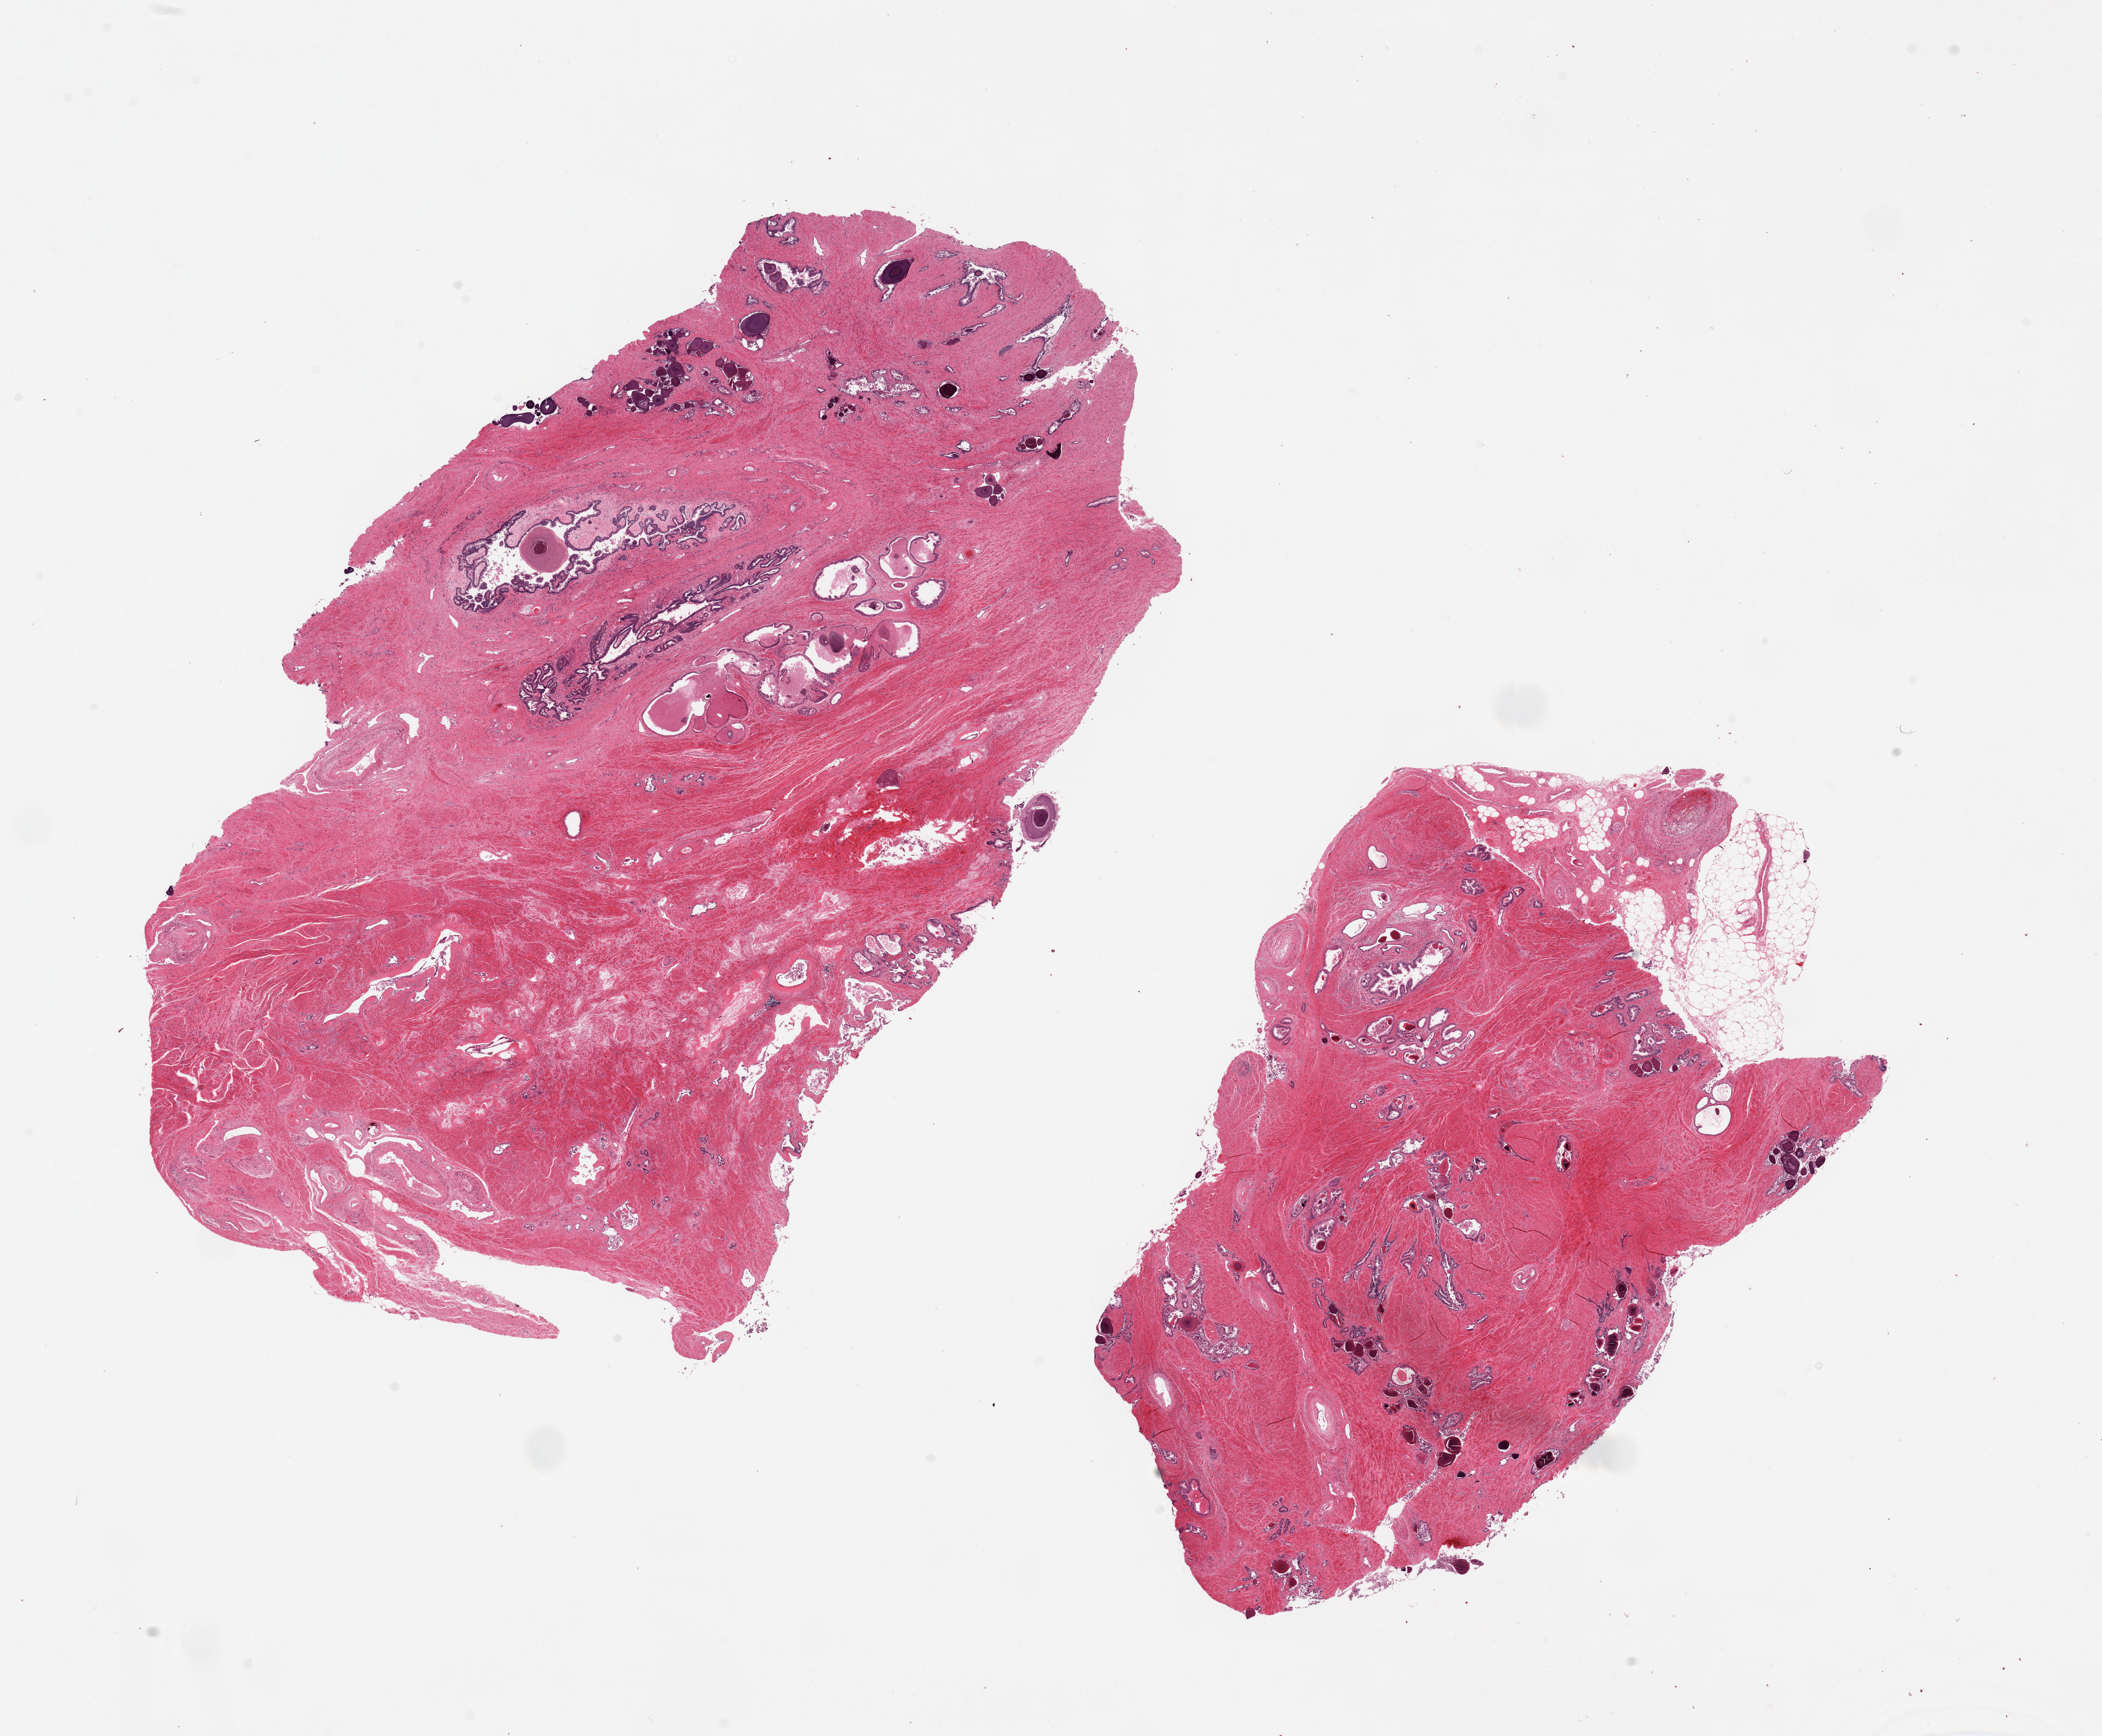
Digitized hematoxylin and eosin (H&E)-stained section, whole scanned area (about 24.6 x 20.3 mm) shown as a low-resolution overview.
Specimen: PAXgene-fixed, paraffin-embedded tissue; sampled site (target tissue): prostate; tissue donor sample.